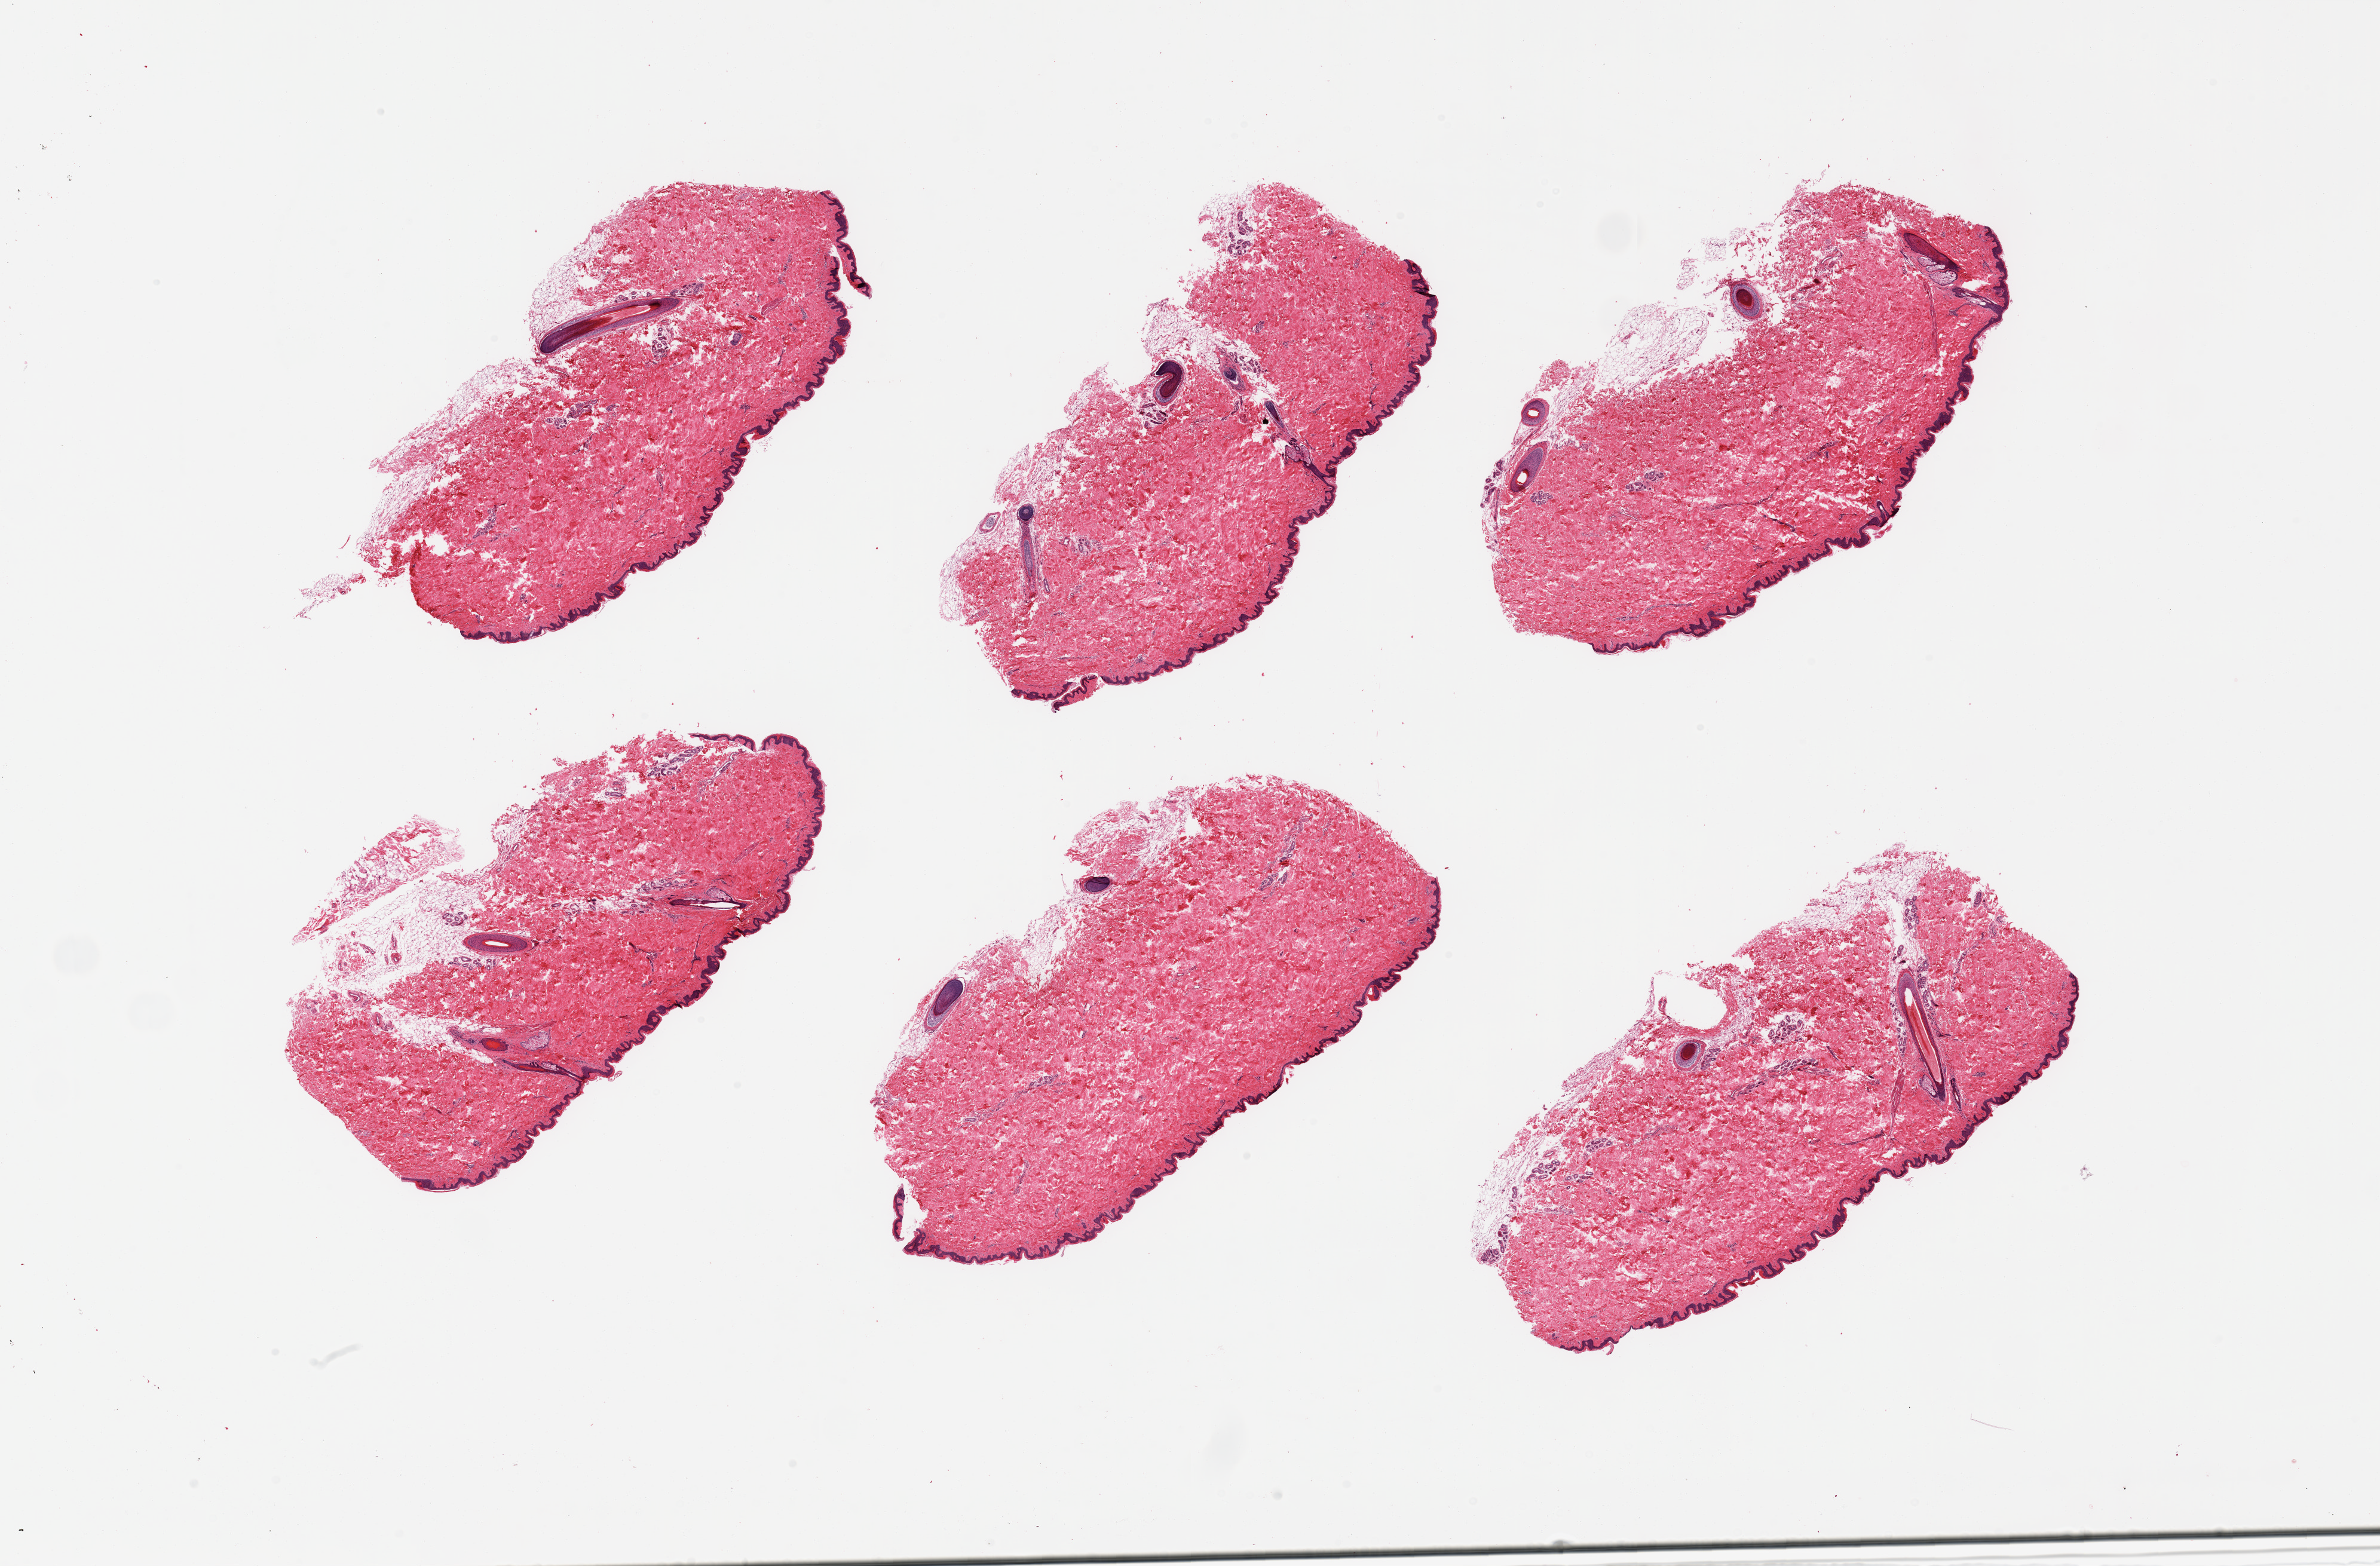
Whole-slide image, hematoxylin and eosin (H&E) stain — whole scanned area (about 31.5 x 20.7 mm) shown as a low-resolution overview, PAXgene-fixed, paraffin-embedded tissue, target tissue: skin of suprapubic region, tissue donor sample. Donor: female.
• pathologist's review note for this sample: 6 pieces, squamous epithelium up to ~50 microns; adherent dermal fat nubbins up to ~1mm